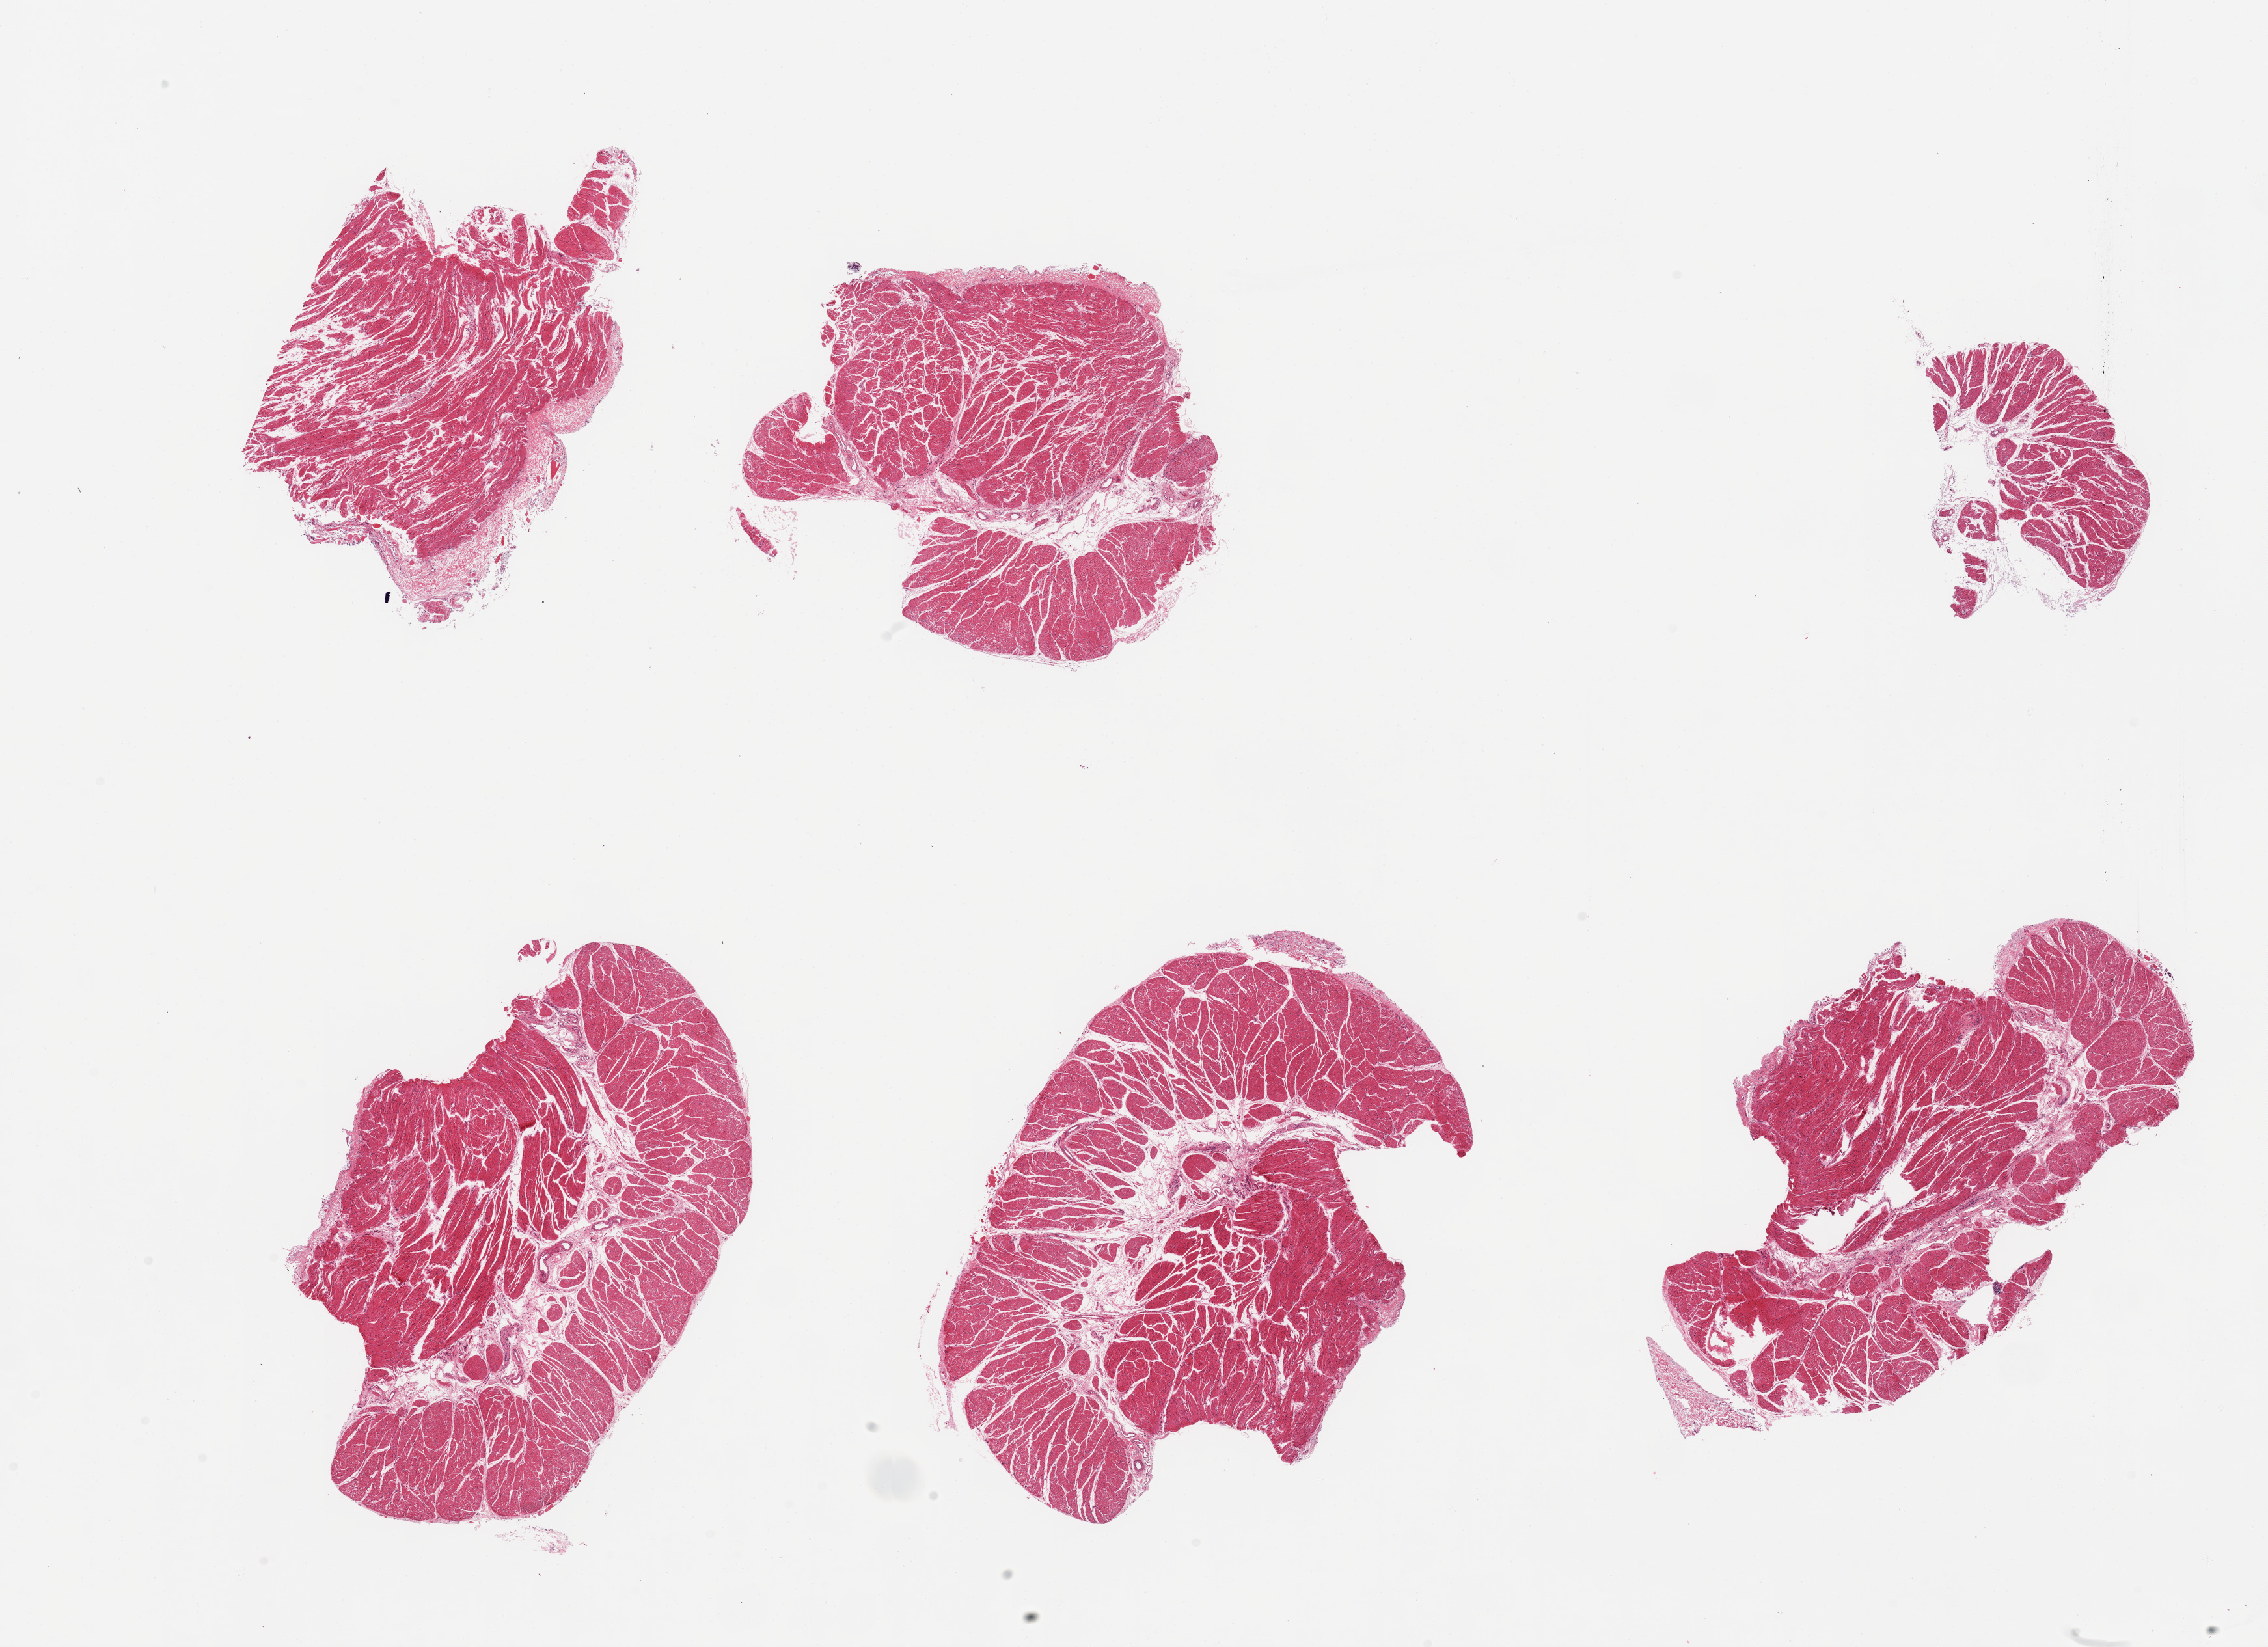
Whole-slide image, H&E stain — whole scanned area (about 27.6 x 20.0 mm, from a 20x scan) shown as a low-resolution overview, PAXgene-fixed, paraffin-embedded tissue, target tissue: esophageal muscle, donor tissue sample. Donor: female.
Pathologist's review note for this sample: 6 pieces; well dissected muscularis.